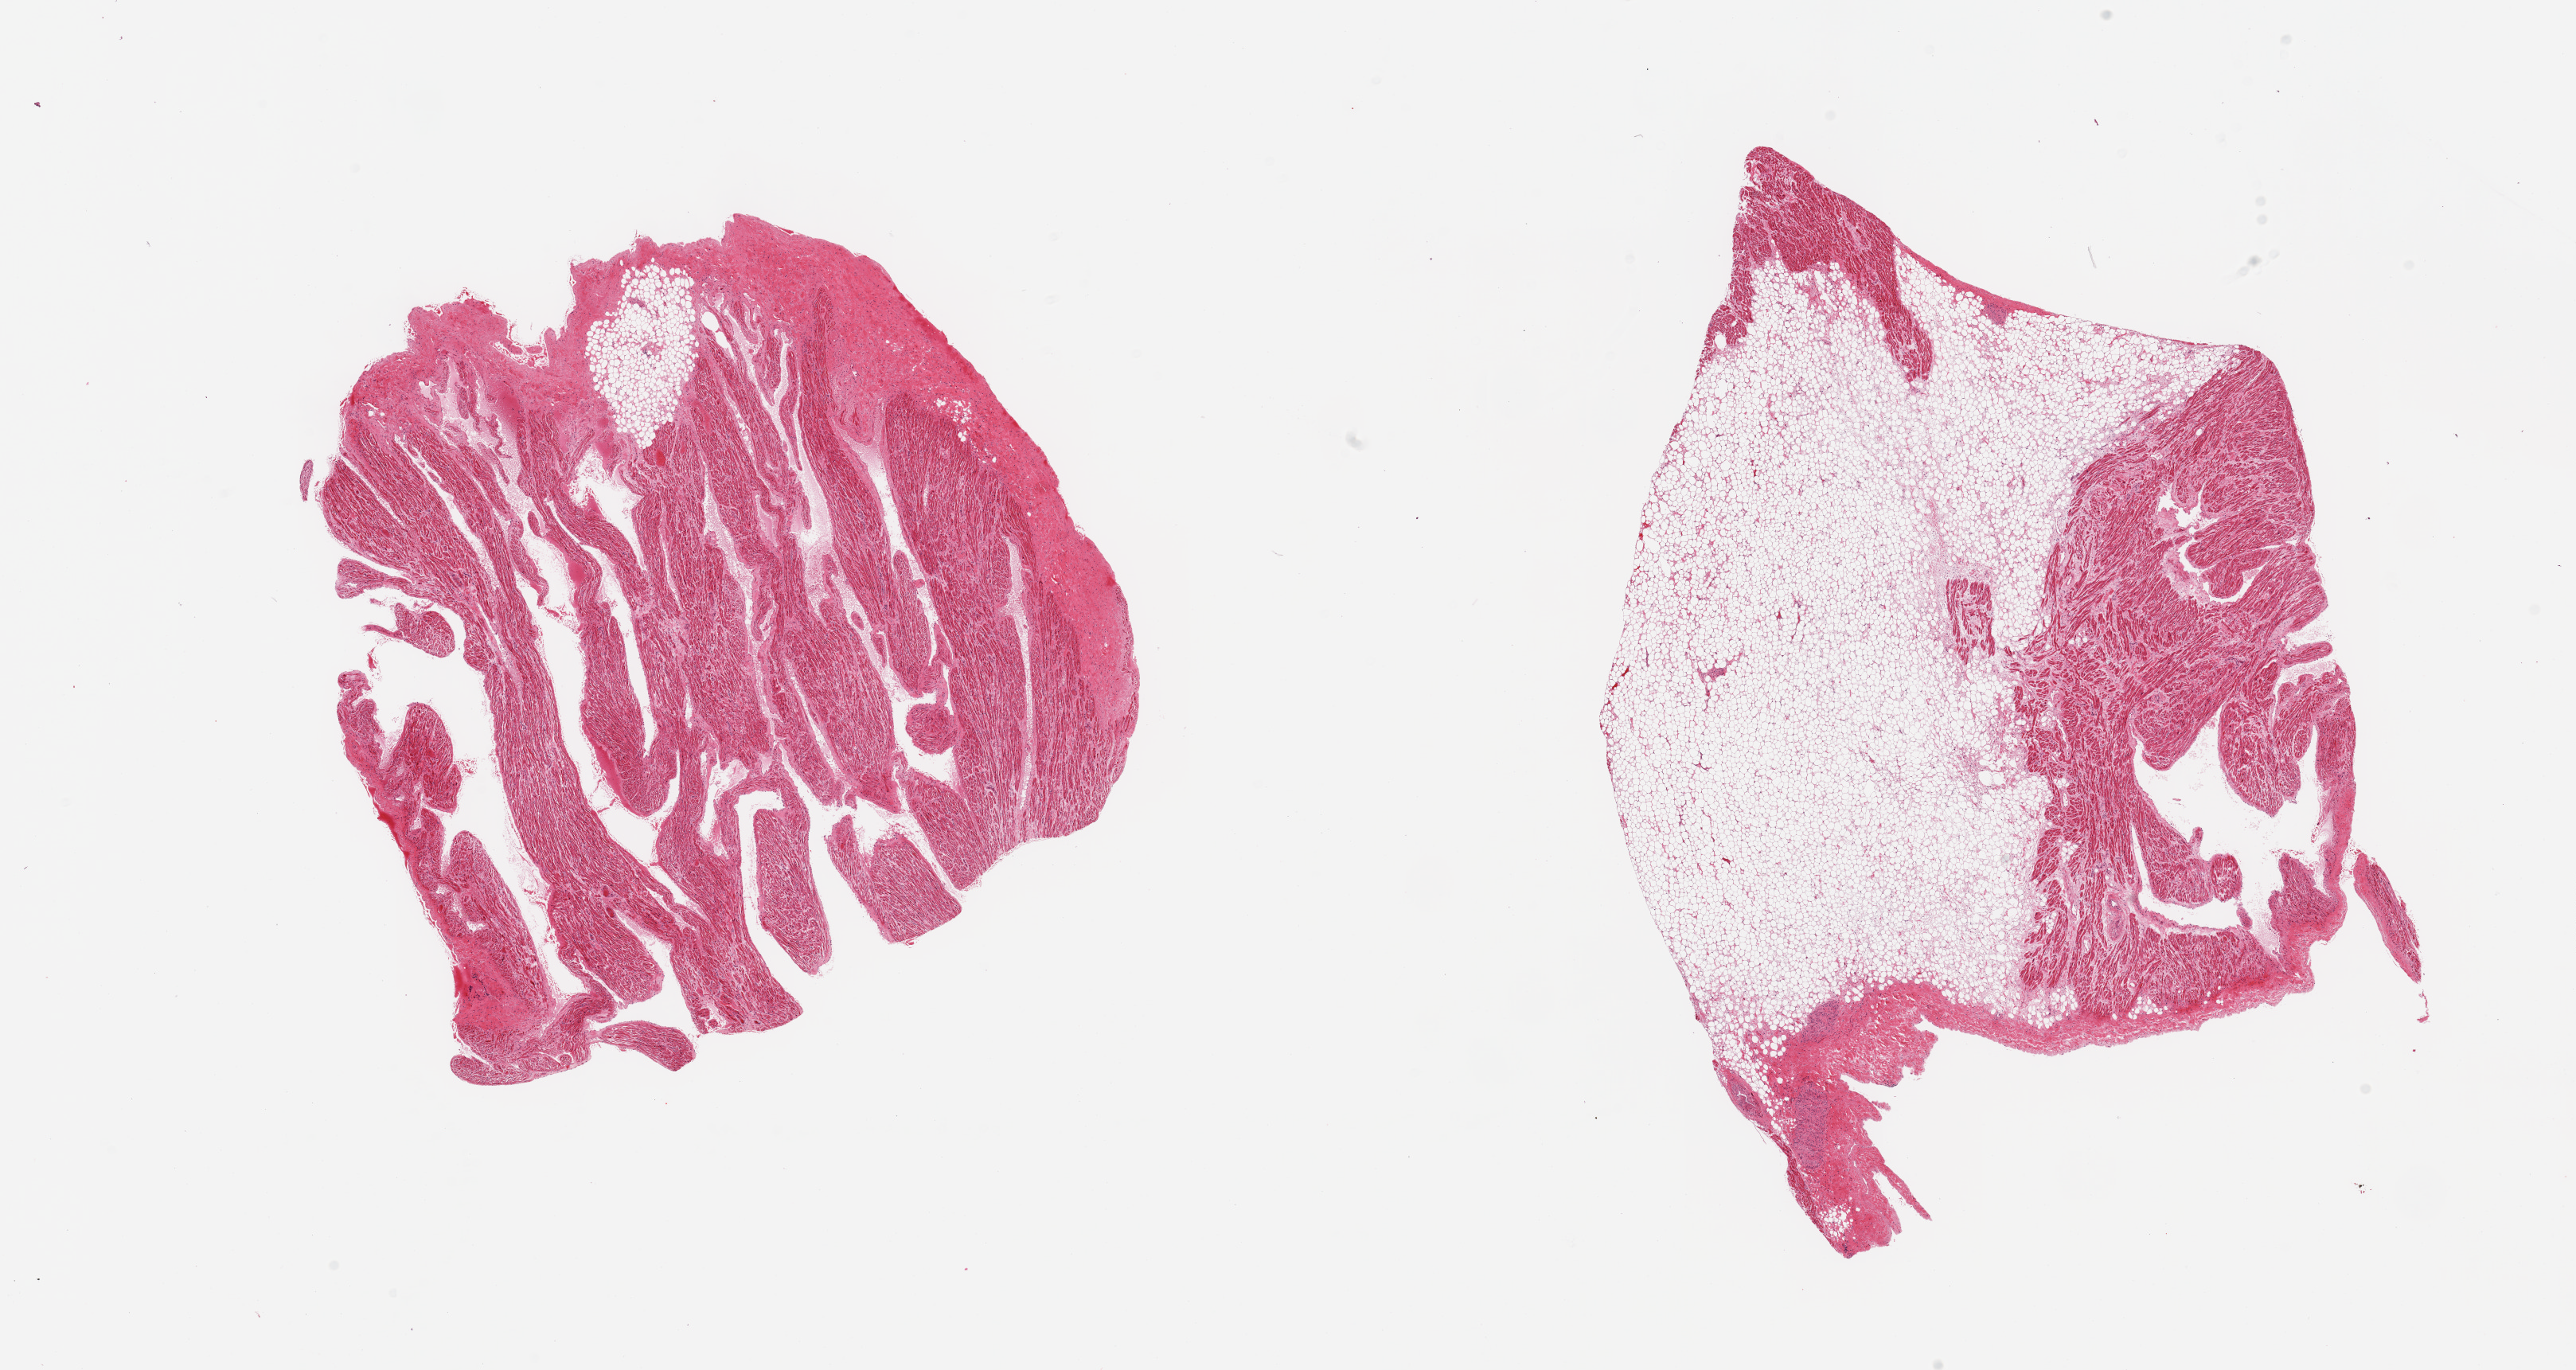
Hematoxylin and eosin (H&E) whole-slide image, whole scanned area (about 25.6 x 13.6 mm) shown as a low-resolution overview. PAXgene-fixed paraffin-embedded (PFPE) section. Sampled site (target tissue): auricular appendage. Donor tissue sample.
Review note (as recorded): 2 pieces; one with <10% internal fat and ~1mm fibrotic band and other with 80% internal fat.